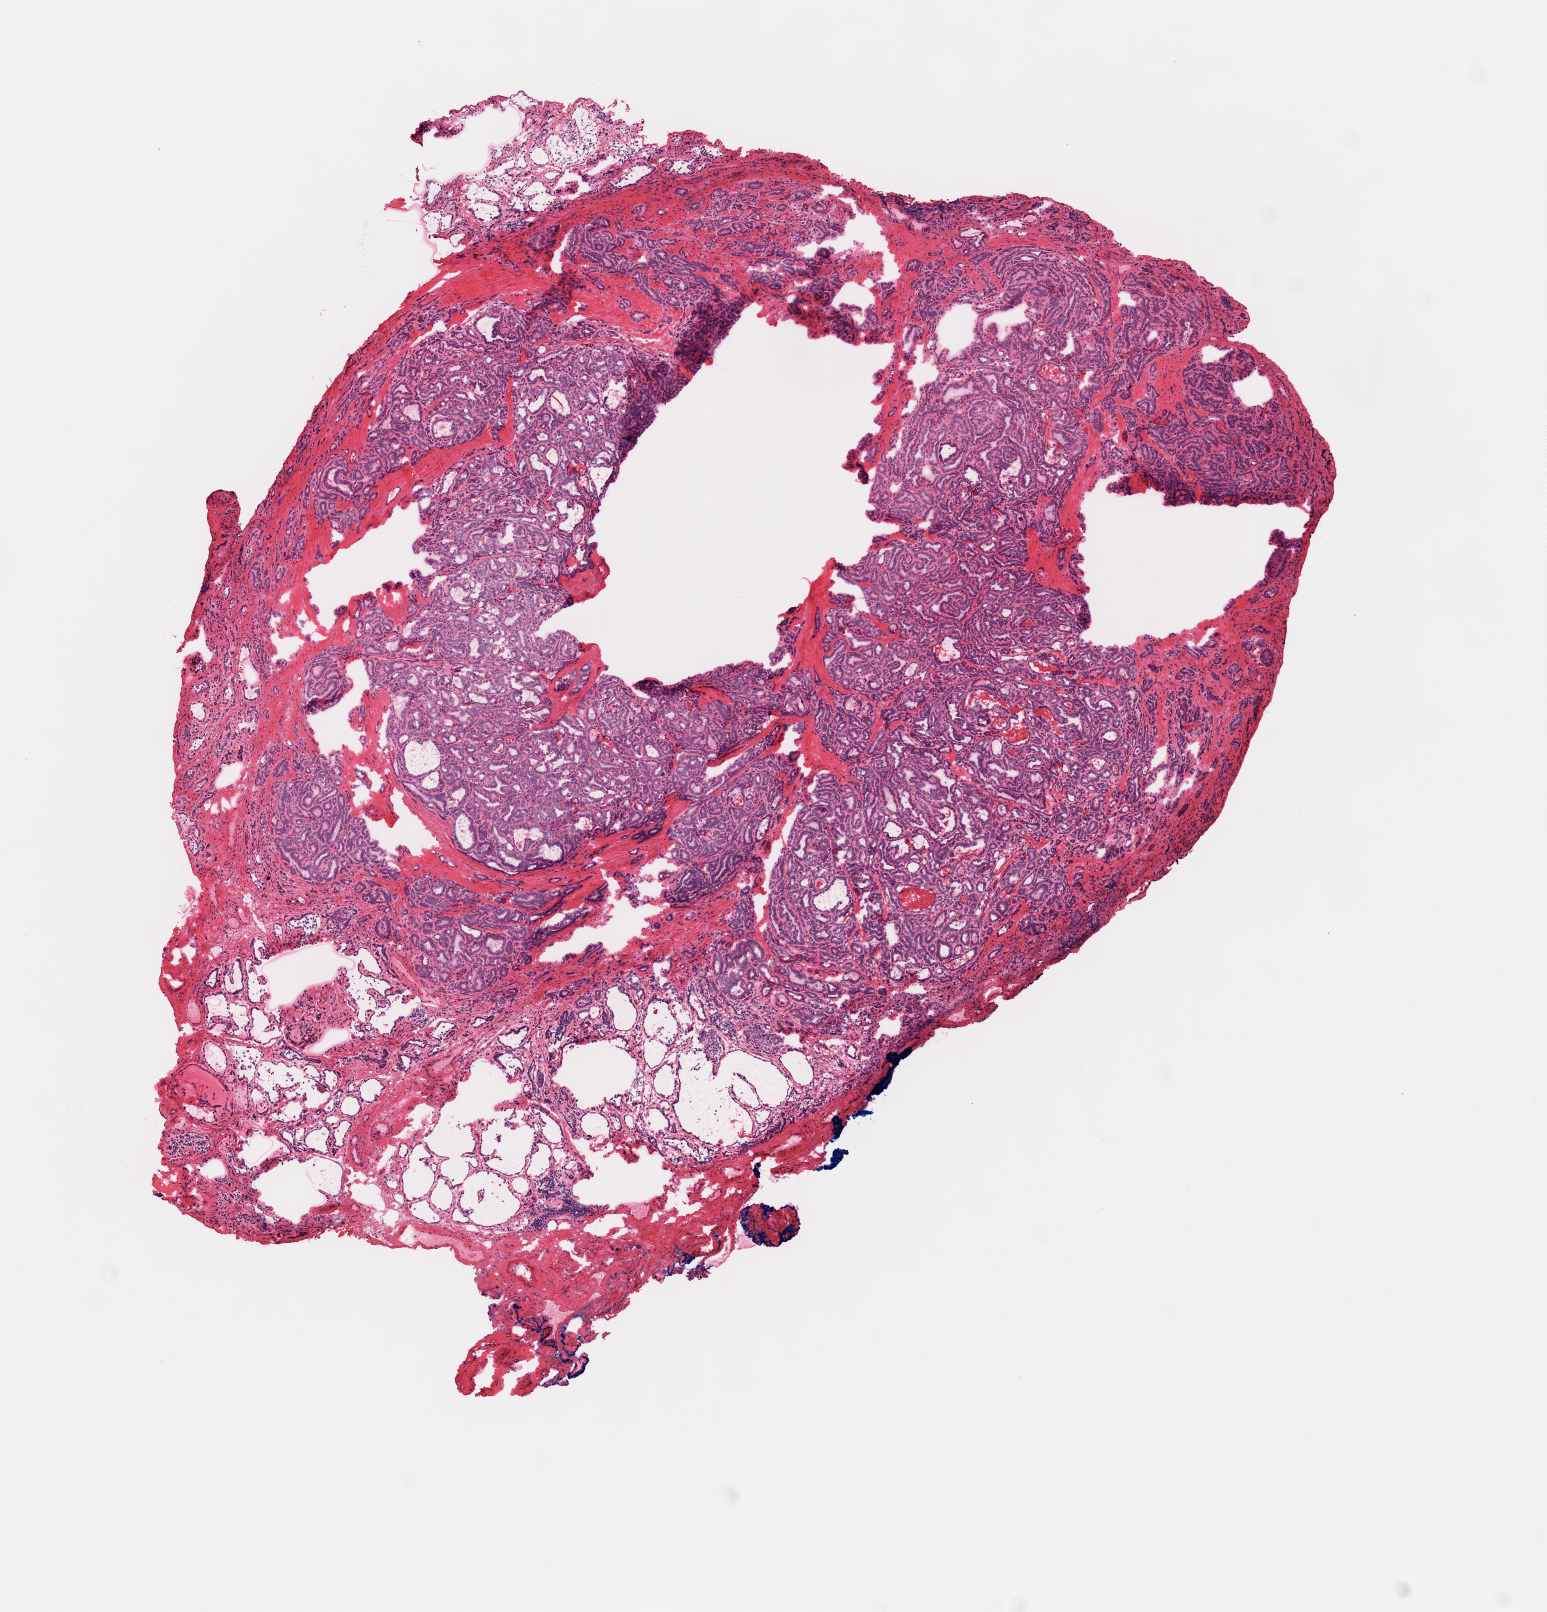
H&E whole-slide image — a low-resolution overview of the entire scanned area, about 6.1 x 6.4 mm (acquisition: 40x scan); frozen section from the top of the tissue portion; primary tumour sample from the thyroid. Female, age 46 years at initial diagnosis.
Diagnosis: Papillary adenocarcinoma, NOS (thyroid gland).